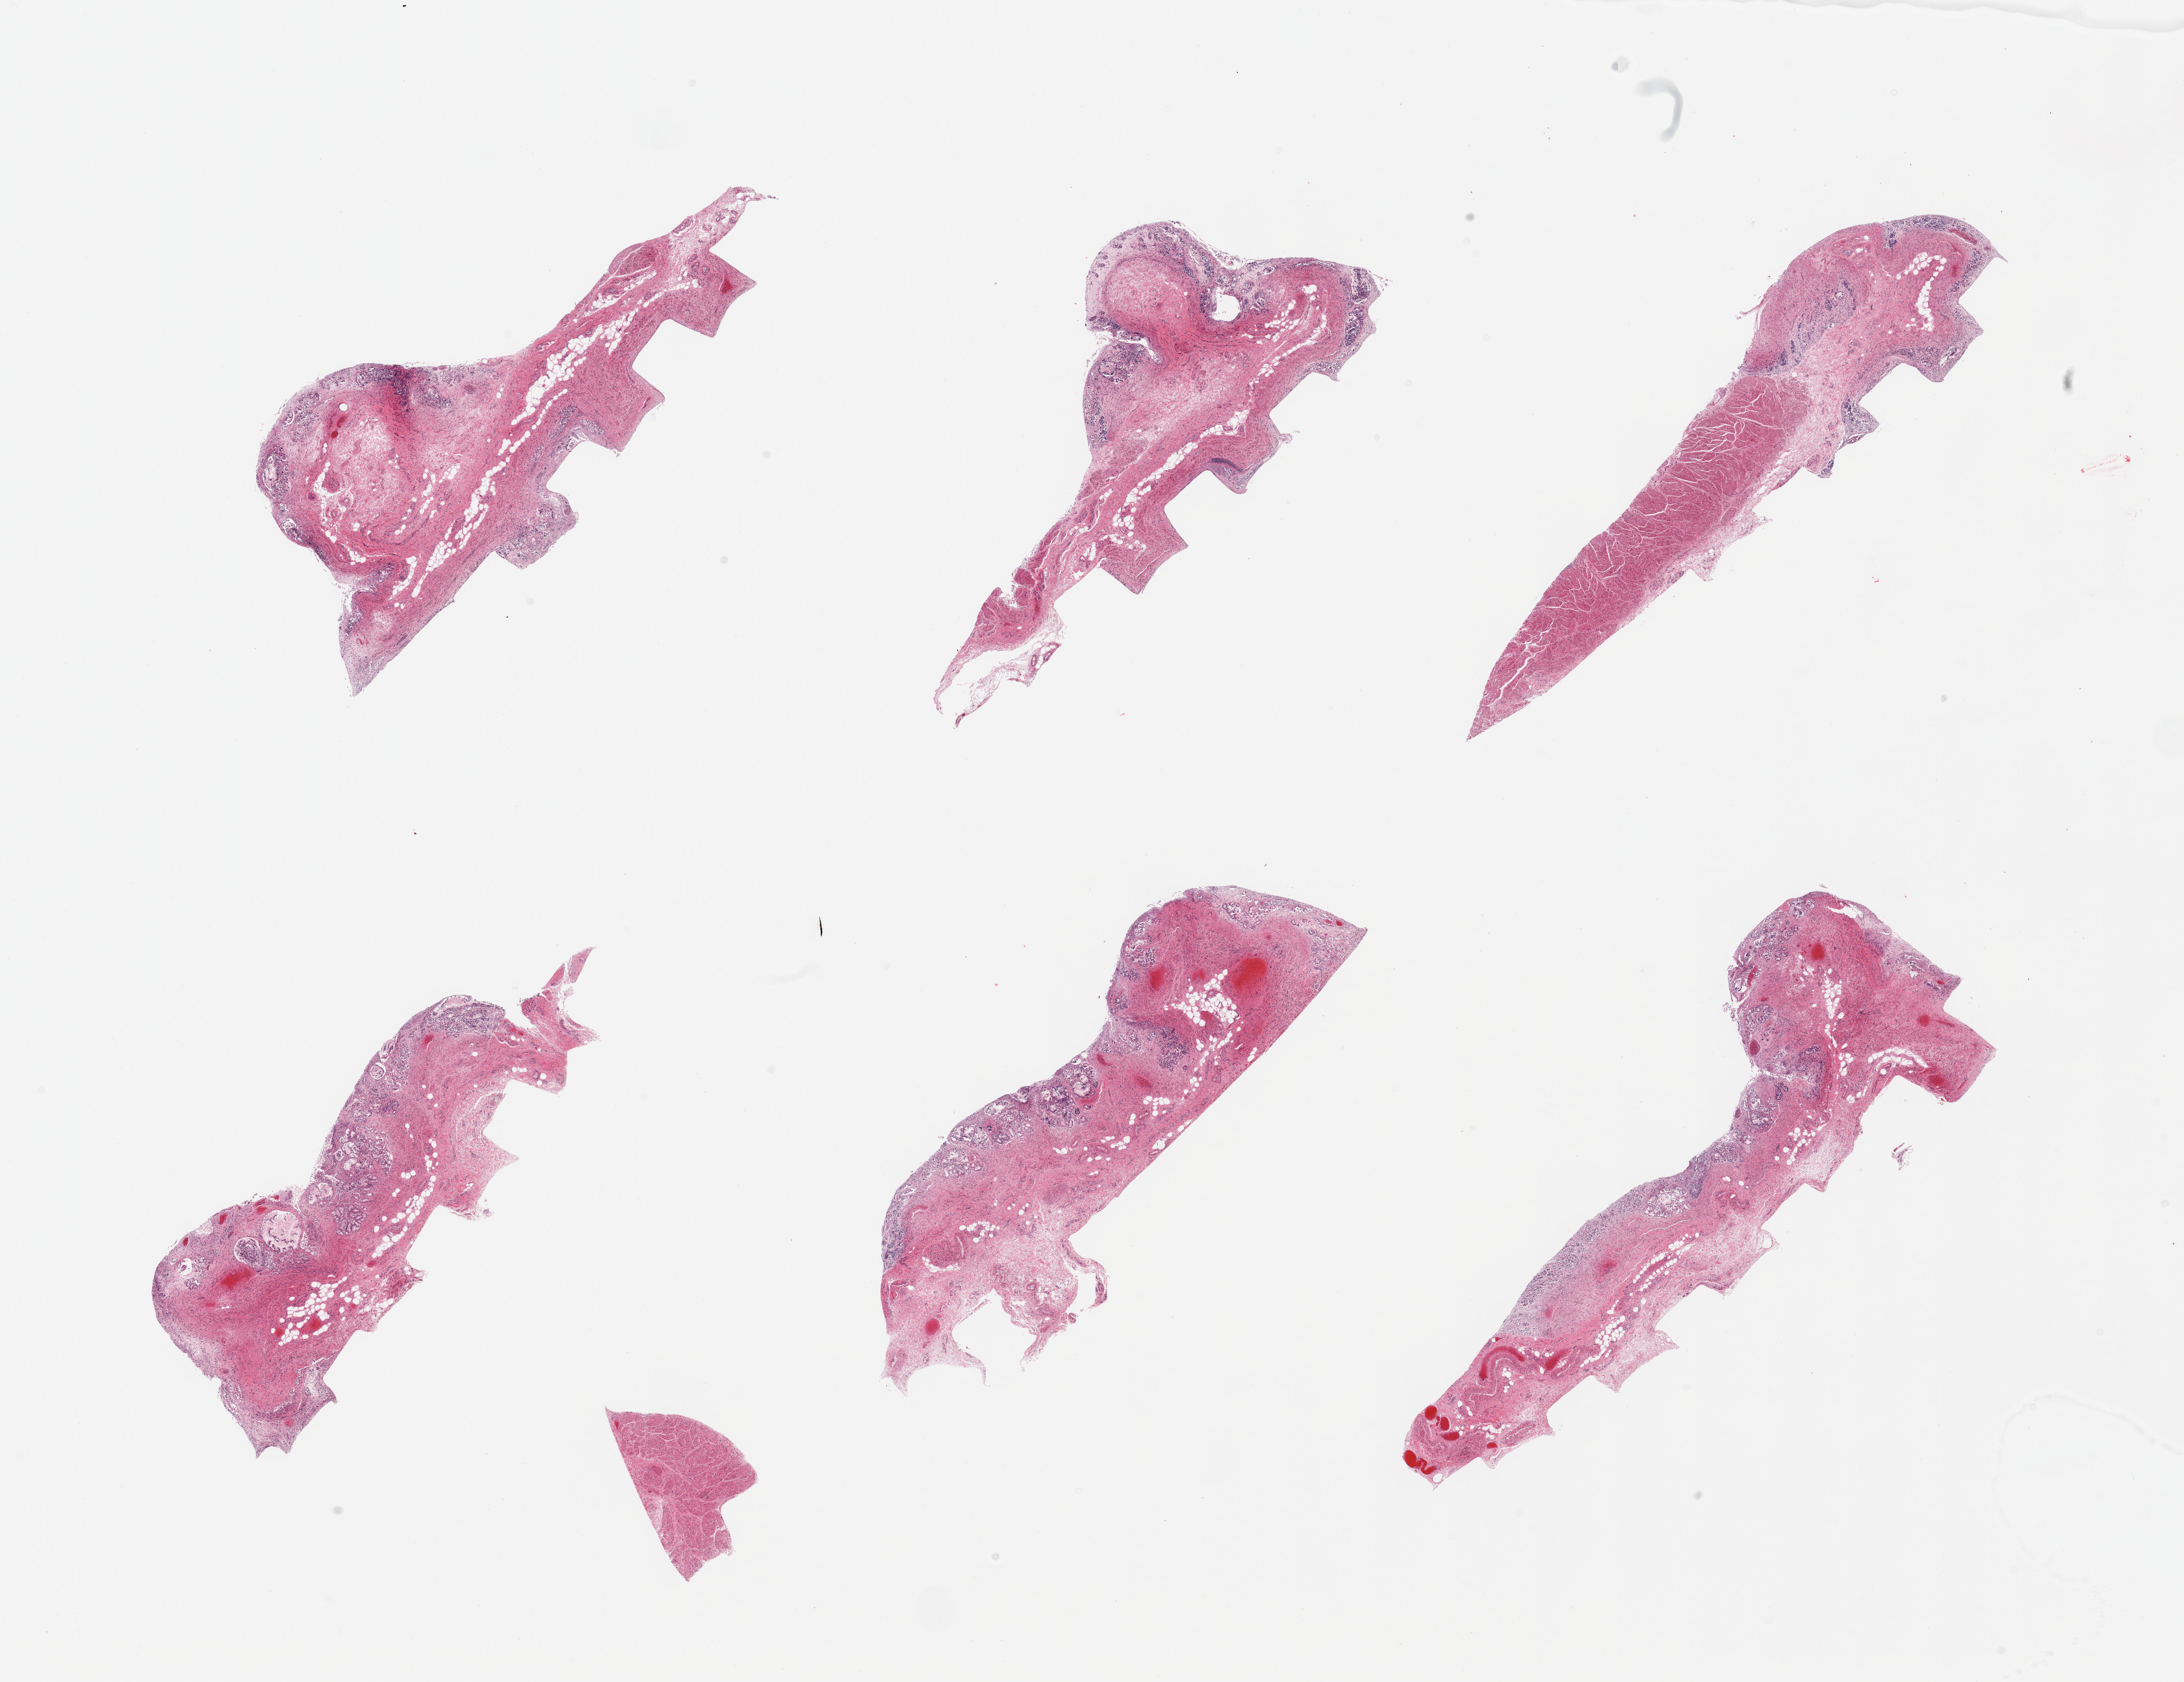
Haematoxylin and eosin whole-slide image, a low-resolution overview of the entire scanned area, about 26.6 x 20.5 mm, PAXgene-fixed paraffin-embedded (PFPE) section, section of esophageal mucous membrane (target tissue), donor tissue sample. Donor sex: male.
Reviewer comment on this tissue sample: 6 pieces; totally autolyzed.